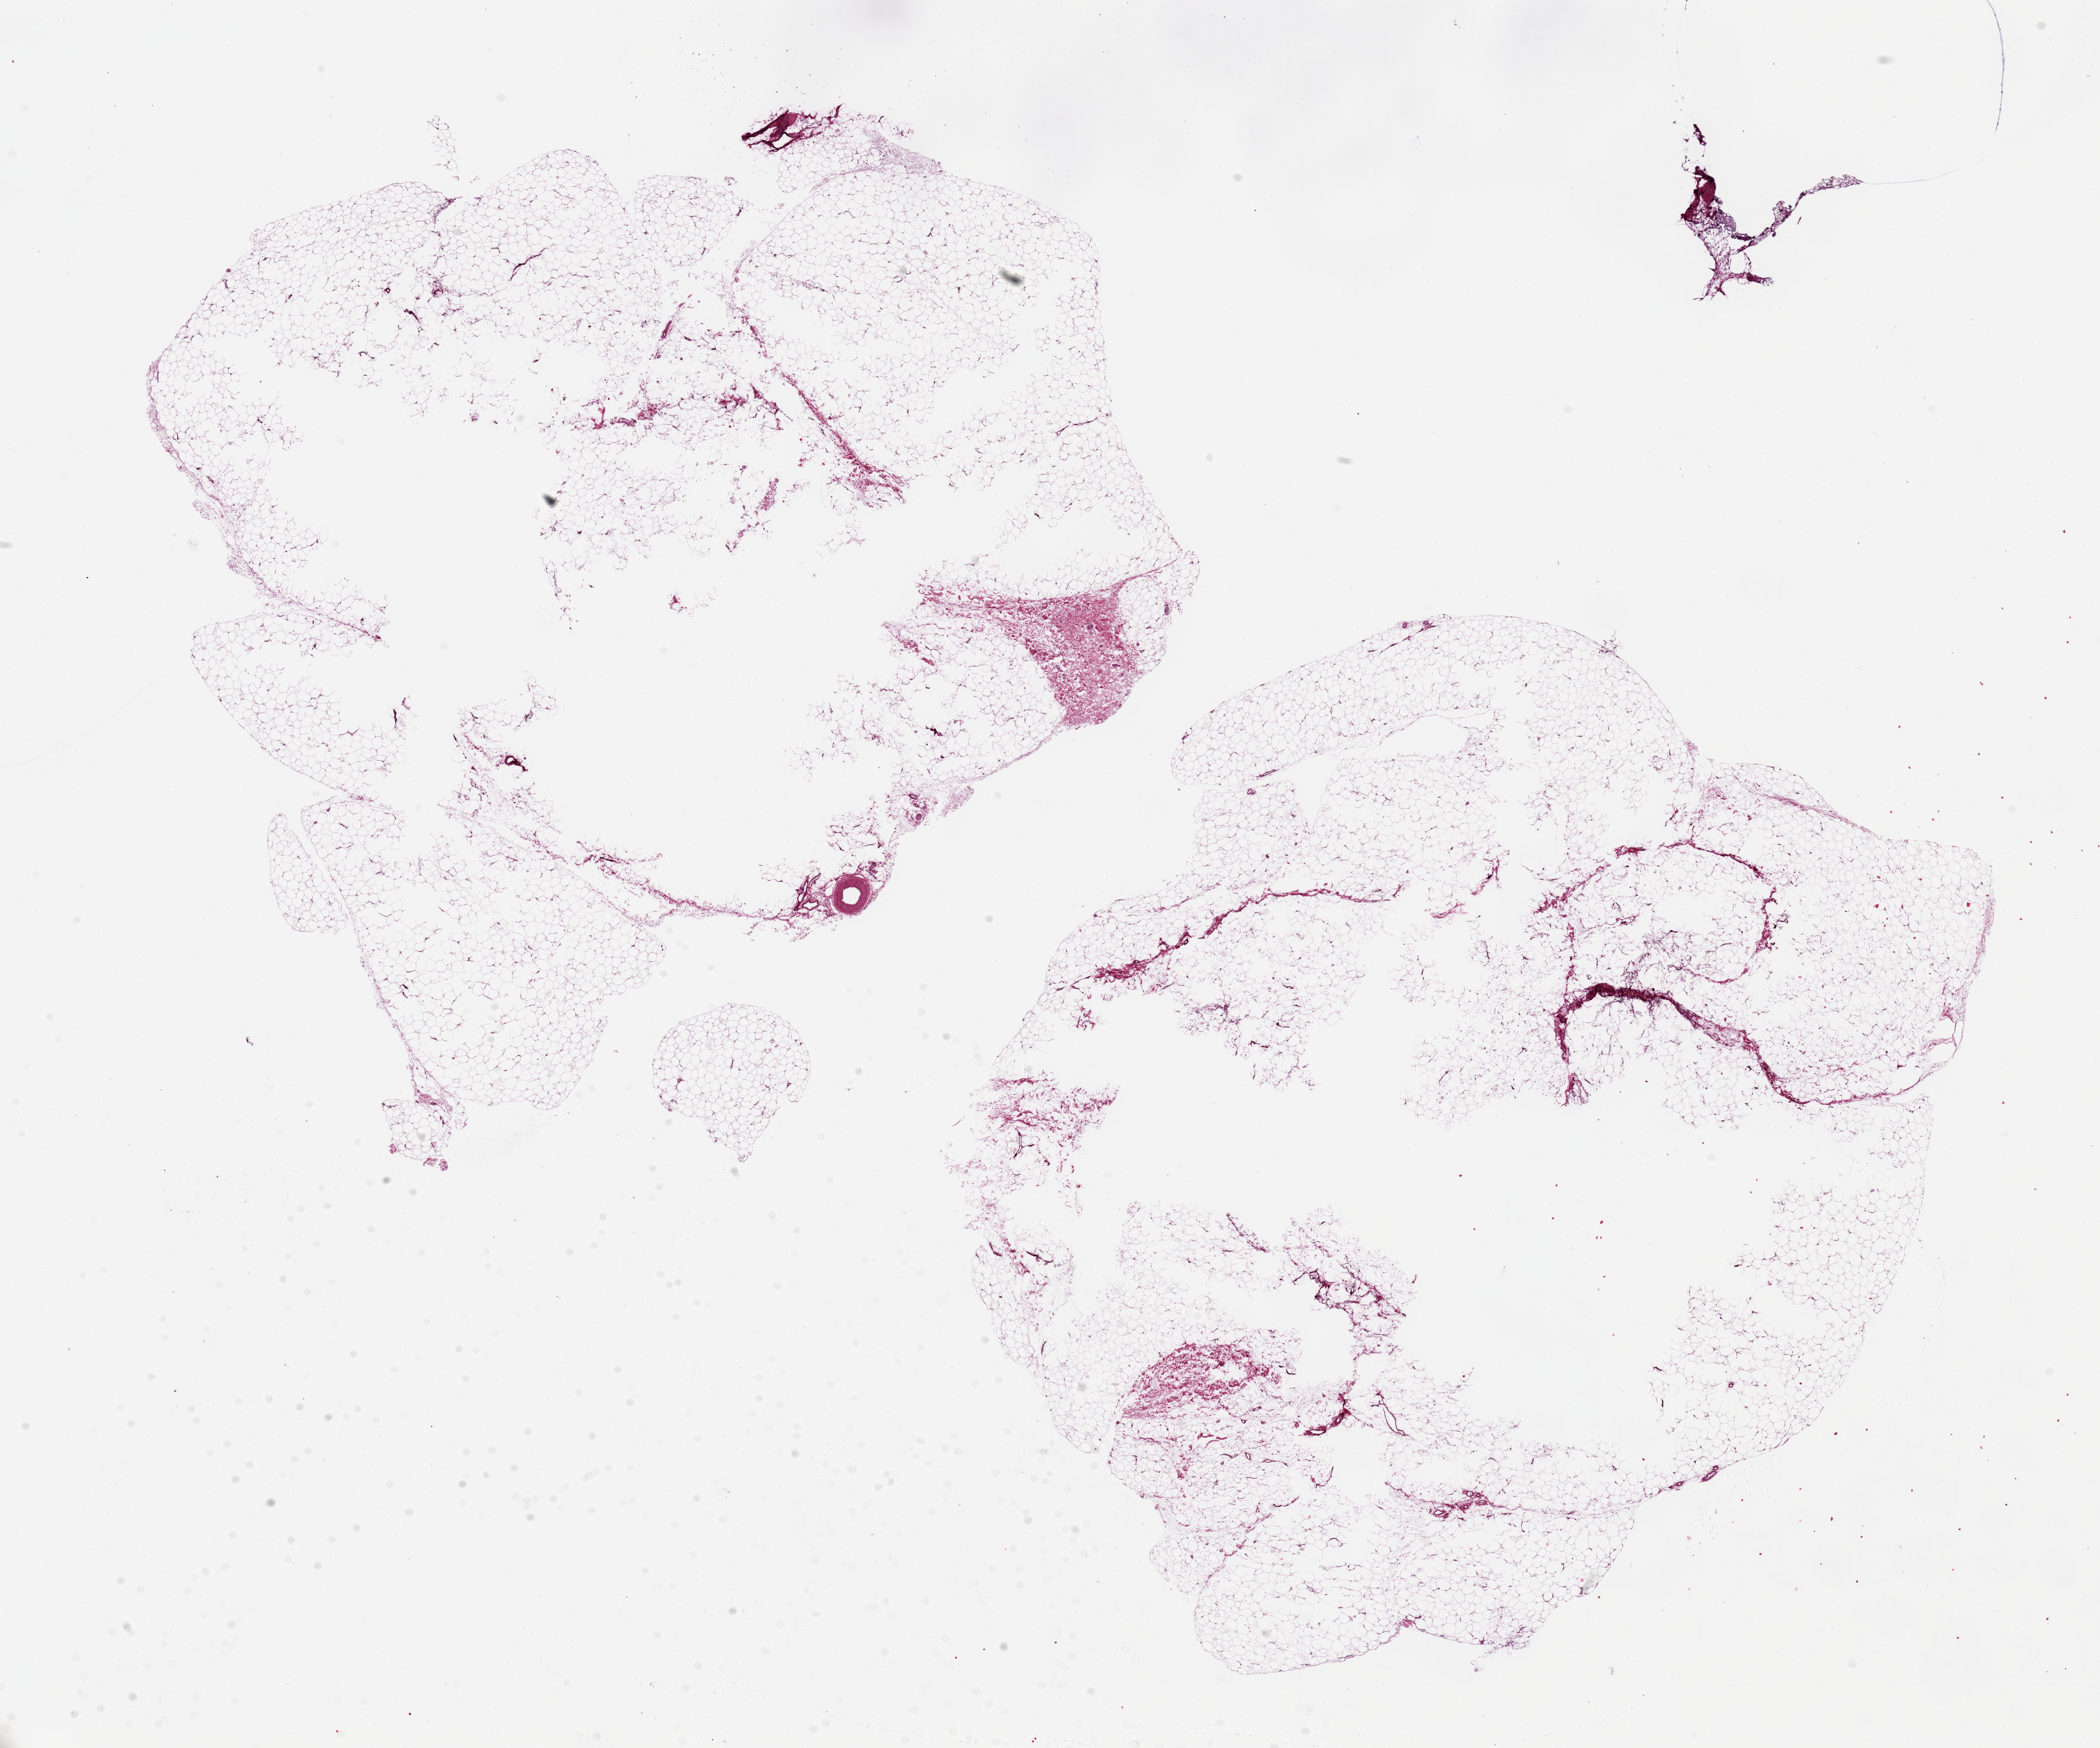
Haematoxylin and eosin whole-slide image, brightfield, a low-resolution overview of the entire scanned area, about 25.6 x 21.3 mm (slide scanned at 20x). PAXgene-fixed paraffin-embedded (PFPE) section. Section of adipose tissue (target tissue). Donor tissue sample. Donor sex: male.
Reviewer comment on this tissue sample: 2 ~ 10x11 mm aliquots, areas of central under-fixation.